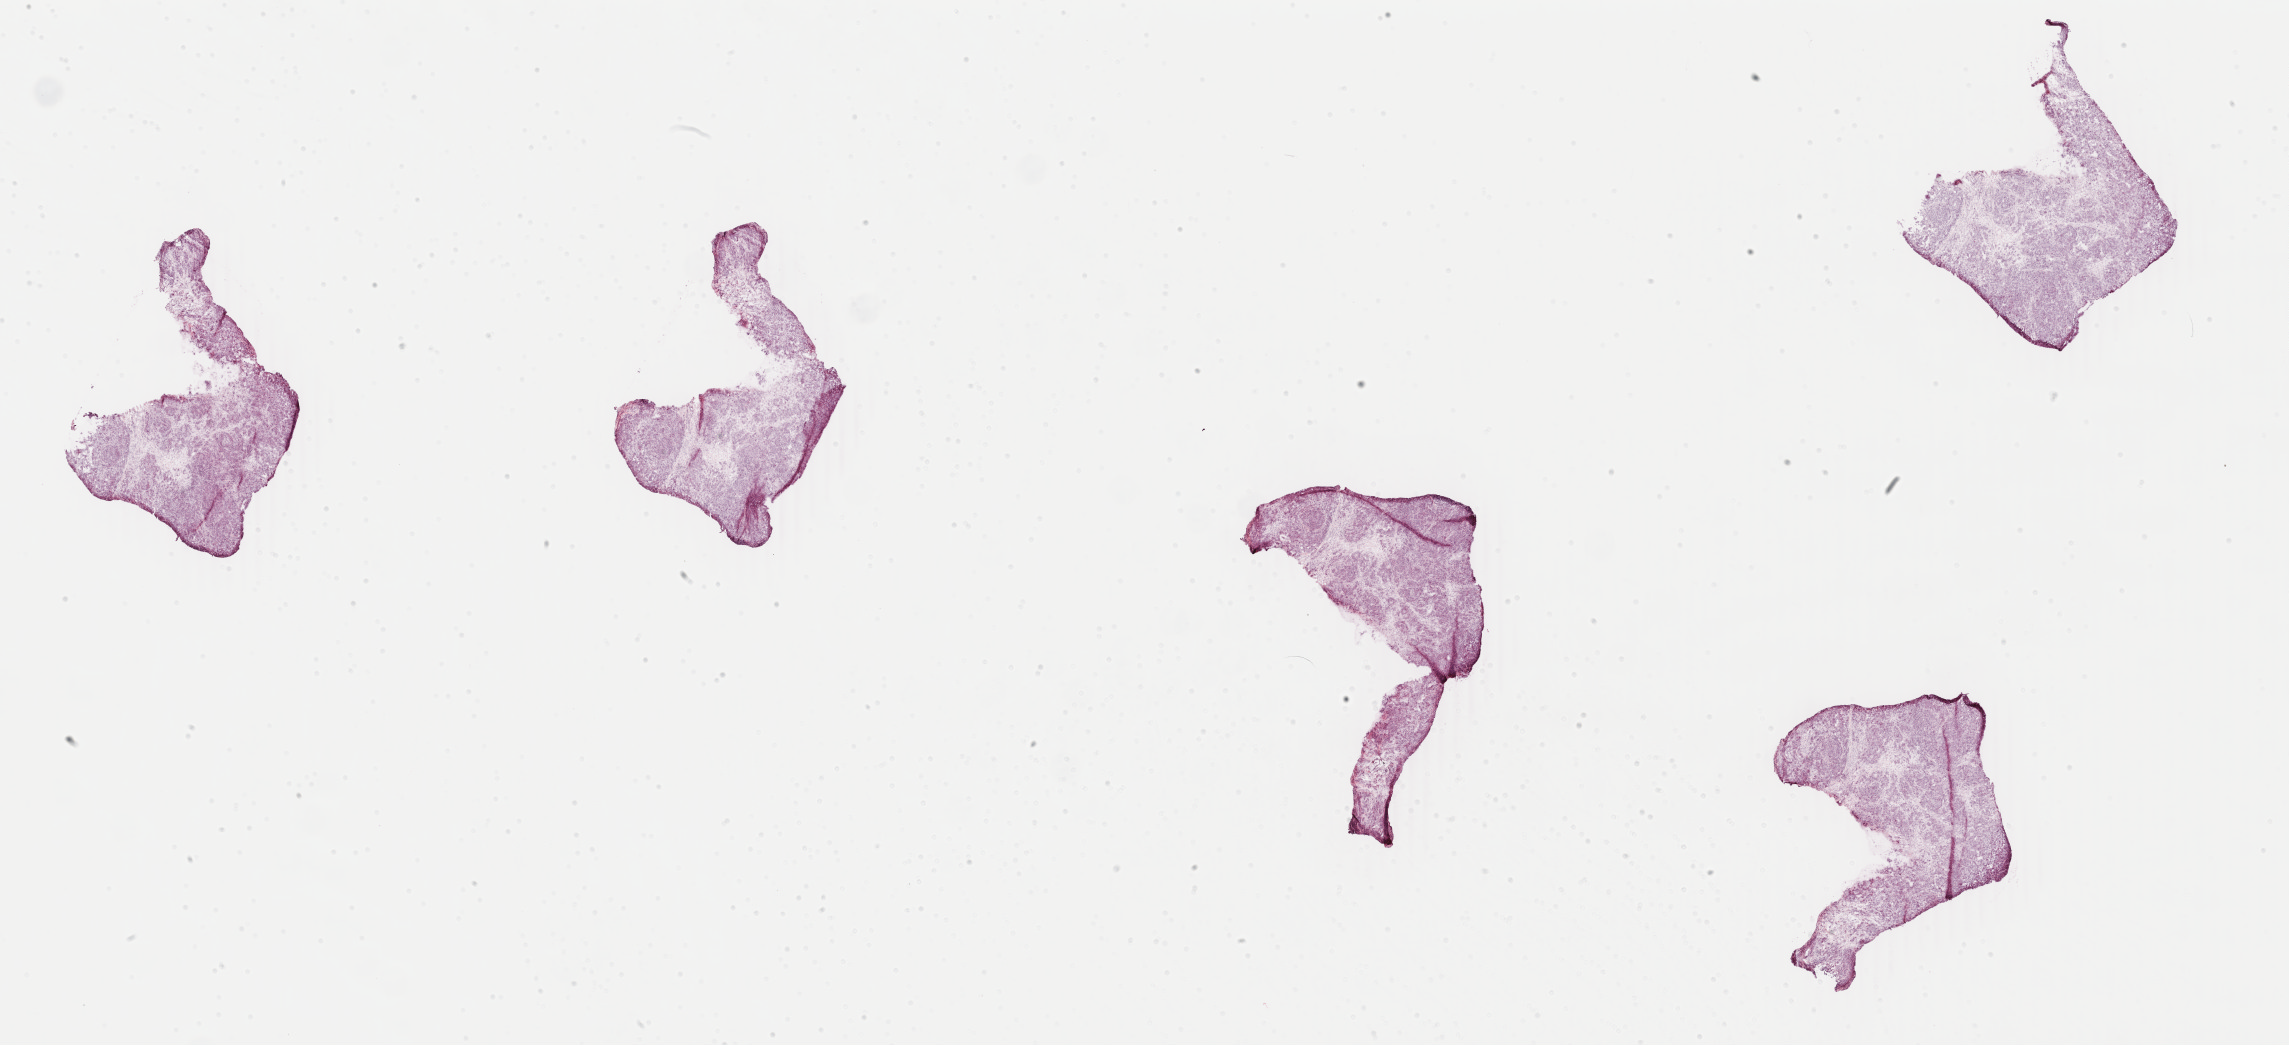
Digitized H&E tissue section (whole slide), whole scanned area (about 36.4 x 16.6 mm, slide scanned at 40x) shown as a low-resolution overview, frozen section from the top of the tissue portion, metastatic tumour sample, sampled site: connective, subcutaneous and other soft tissues. Female patient; age at initial diagnosis 46 years.
This section: metastatic tumour tissue. Patient diagnosis: Malignant melanoma, NOS.